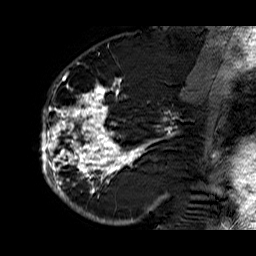
Breast MRI (dynamic contrast-enhanced), one sagittal slice. Slice 36 of 60 in the series (ordered by position). Dynamic contrast-enhanced series, time point 2 of 6 at this slice position (early post-contrast). 1.5 T. TE 6.3 ms, TR 32.9 ms. 4 mm slice thickness. 256 × 256 image matrix, field of view 200 × 200 mm. Female patient. From the clinical record (not read from this slice): setting: breast cancer imaged before/during neoadjuvant chemotherapy; receptor status: HR-positive, HER2-negative.
Outlined on this slice (semi-automatically segmented with operator editing):
- analysis volume of interest (the breast-tissue region the enhancement analysis was run in; not a lesion): box from (x=39, y=74) to (x=176, y=210) px
- tumour enhancement mask (voxels above the 100 % enhancement threshold inside the analysis volume of interest): (x=40, y=75)–(x=170, y=210)